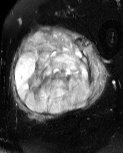
MRI of an extremity soft-tissue mass, one axial slice; position 24 of 60 along the scan axis; T2-weighted fat-saturated; MR volume resampled by the dataset authors to the PET/CT grid (not the native acquisition matrix); 123 × 153 image matrix, field of view 120 × 149 mm. Male patient. From the clinical record (not read from this slice): histological type: pleiomorphic liposarcoma; grade: high; site of the primary tumour: left thigh.
Annotated regions visible in this slice (expert contour drawn on MRI and transferred to this co-registered scan by the dataset authors):
- gross tumour volume including surrounding oedema: bounding box [x1, y1, x2, y2] px = [11, 27, 110, 121]
- gross tumour volume (mass): [15, 31, 94, 114]